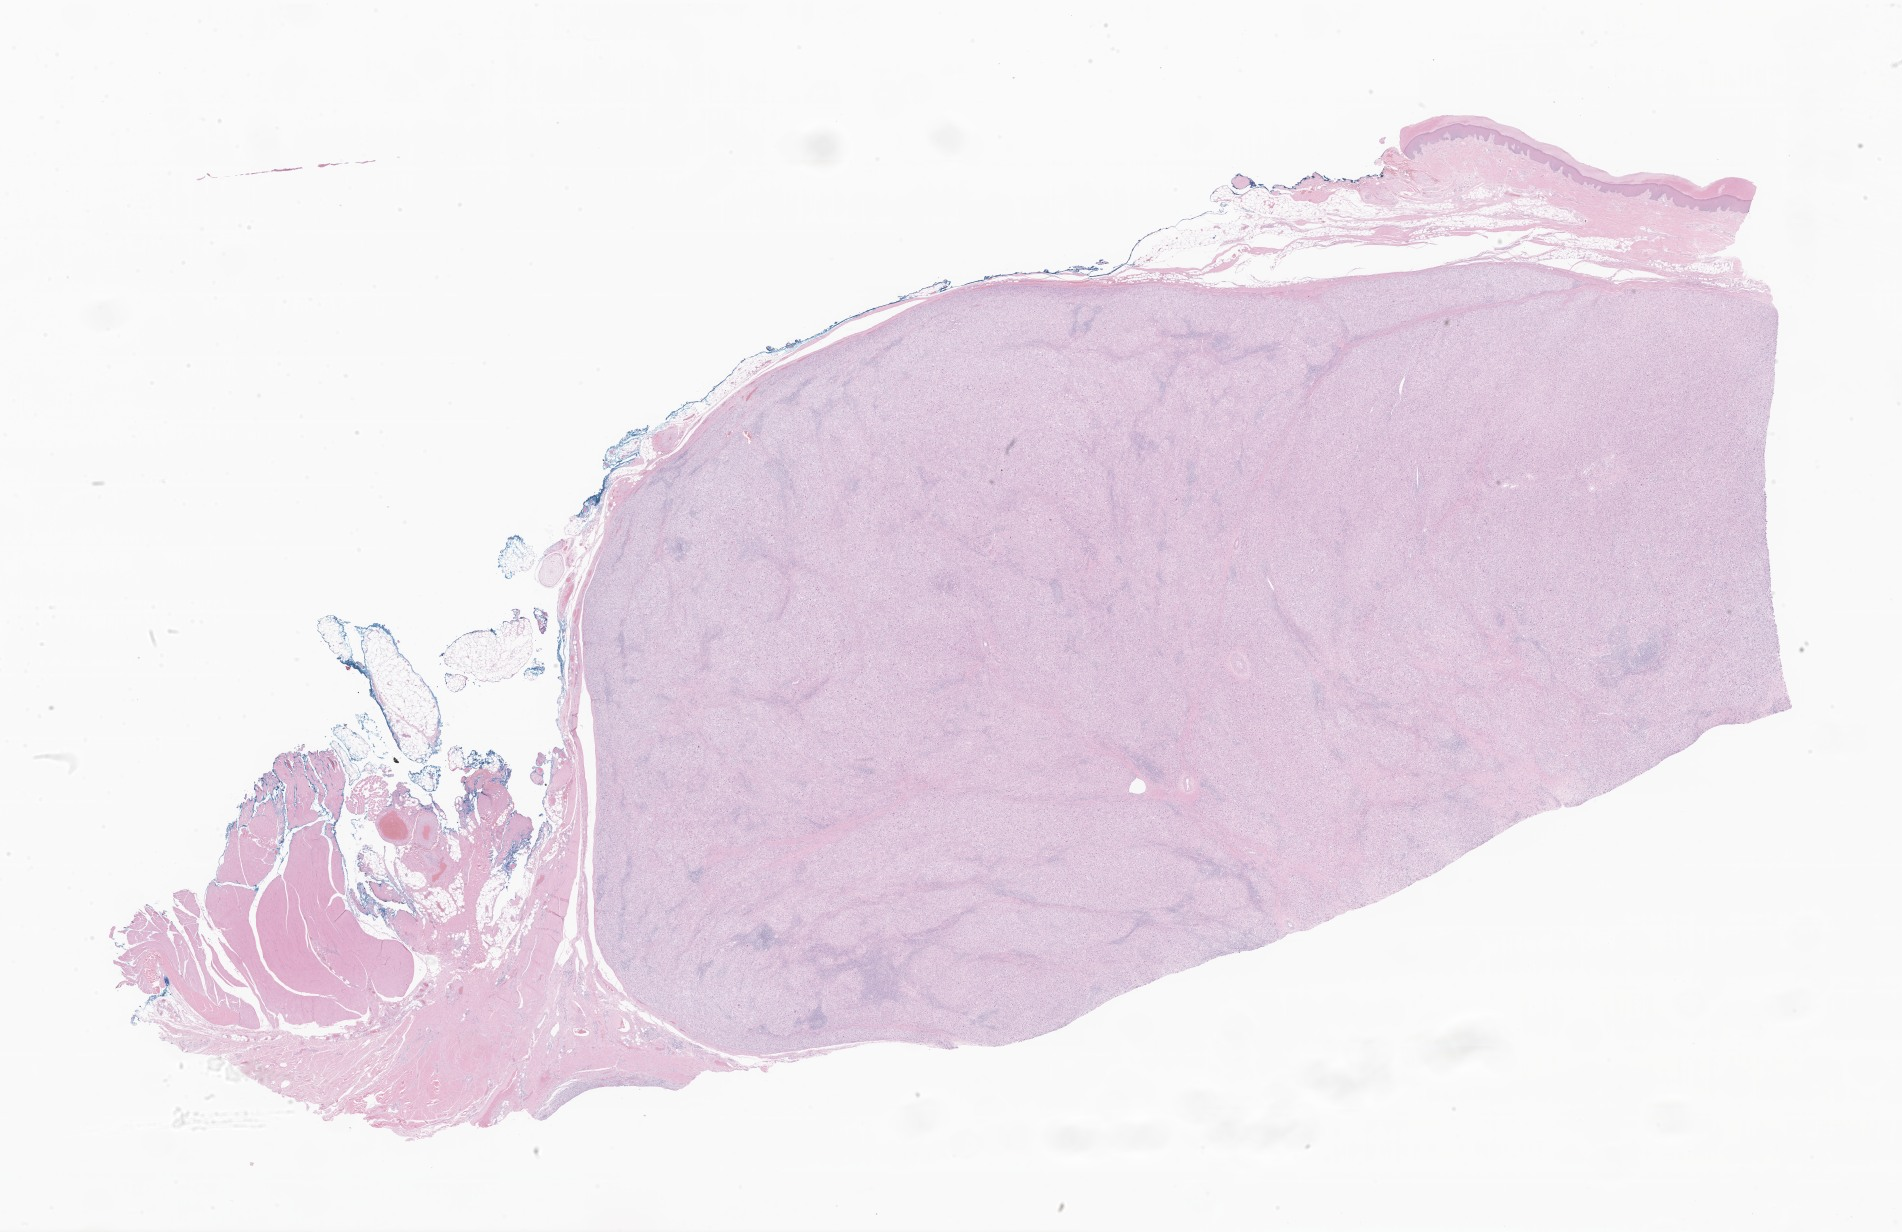
Whole-slide image, H&E stain of tumor tissue from the soft tissue of upper extremity — a low-resolution overview of the entire scanned area, about 32.1 x 20.8 mm; formalin-fixed paraffin-embedded section. Patient female; age 204 months (17 years).
- recorded diagnosis: Neoplasm, malignant